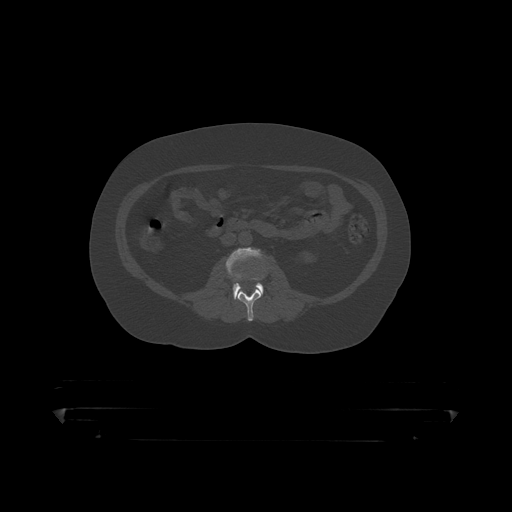
CT including the spine, one axial slice; slice 105 of 390 in the series (ordered by position); reconstruction kernel STANDARD; bone window (W 1800 / L 400 HU); 512 × 512 image matrix, field of view 650 × 650 mm. Male patient, age 60 years. Case-level facts recorded for this patient, not image findings: primary cancer: prostate.
Outlined on this slice (semi-automatically segmented with operator editing):
- L2 vertebra: bounding box [x1, y1, x2, y2] px = [238, 273, 267, 319]
- L3 vertebra: [227, 248, 264, 299]